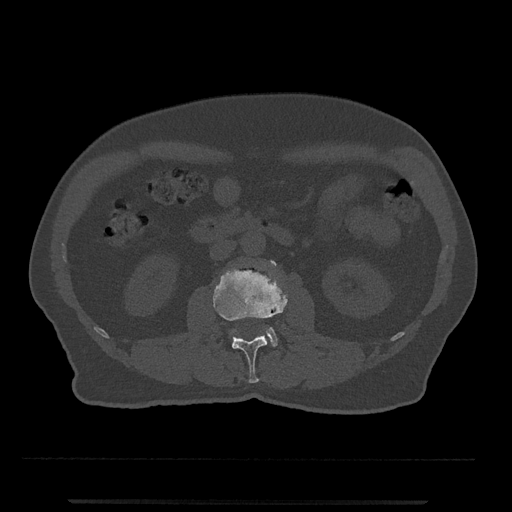
CT including the spine, one axial slice. Slice 248 of 797 in the series (ordered by position). Reconstruction kernel Br40s/3. 120 kVp. Bone window (W 1800 / L 400 HU). 0.5 mm slice thickness. 512 × 512 image matrix, field of view 419 × 419 mm. Male patient, age 63 years. From the clinical record (not read from this slice): primary cancer: prostate.
Annotated regions visible in this slice (semi-automatic segmentation, software-assisted and operator-edited):
- L2 vertebra: bounding box [x1, y1, x2, y2] px = [213, 261, 288, 383]
- L3 vertebra: [266, 260, 278, 347]